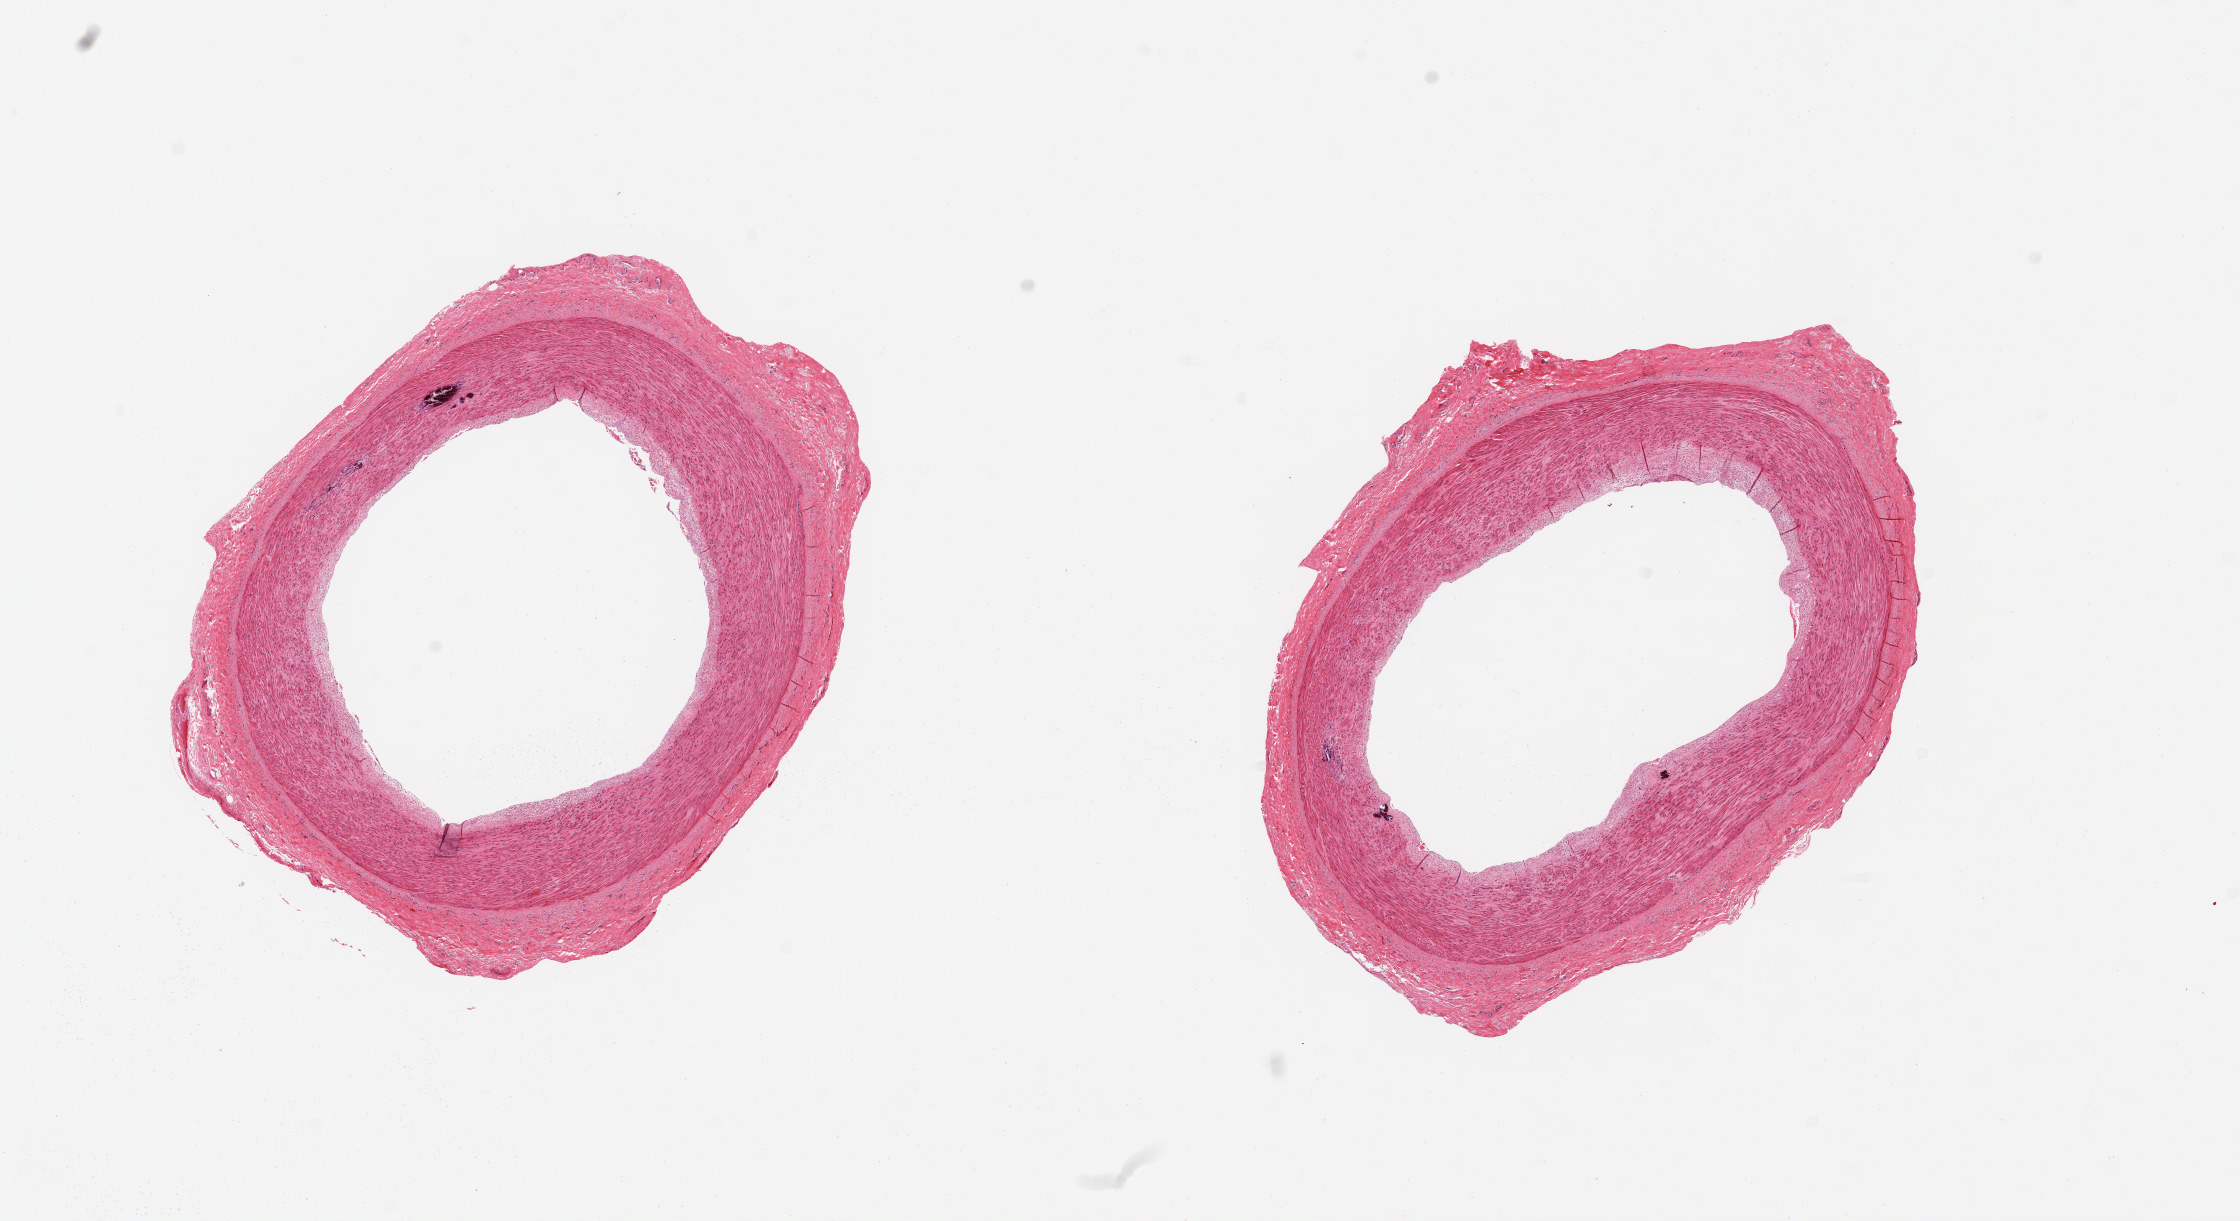
Whole-slide image, haematoxylin and eosin stain, whole scanned area (about 17.7 x 9.7 mm) shown as a low-resolution overview; PAXgene-fixed, paraffin-embedded tissue; target tissue: tibial artery; donor tissue sample.
- review note (as recorded): 2 pieces; minimal intimal thickening; several small calcium deposits in media; well trimmed